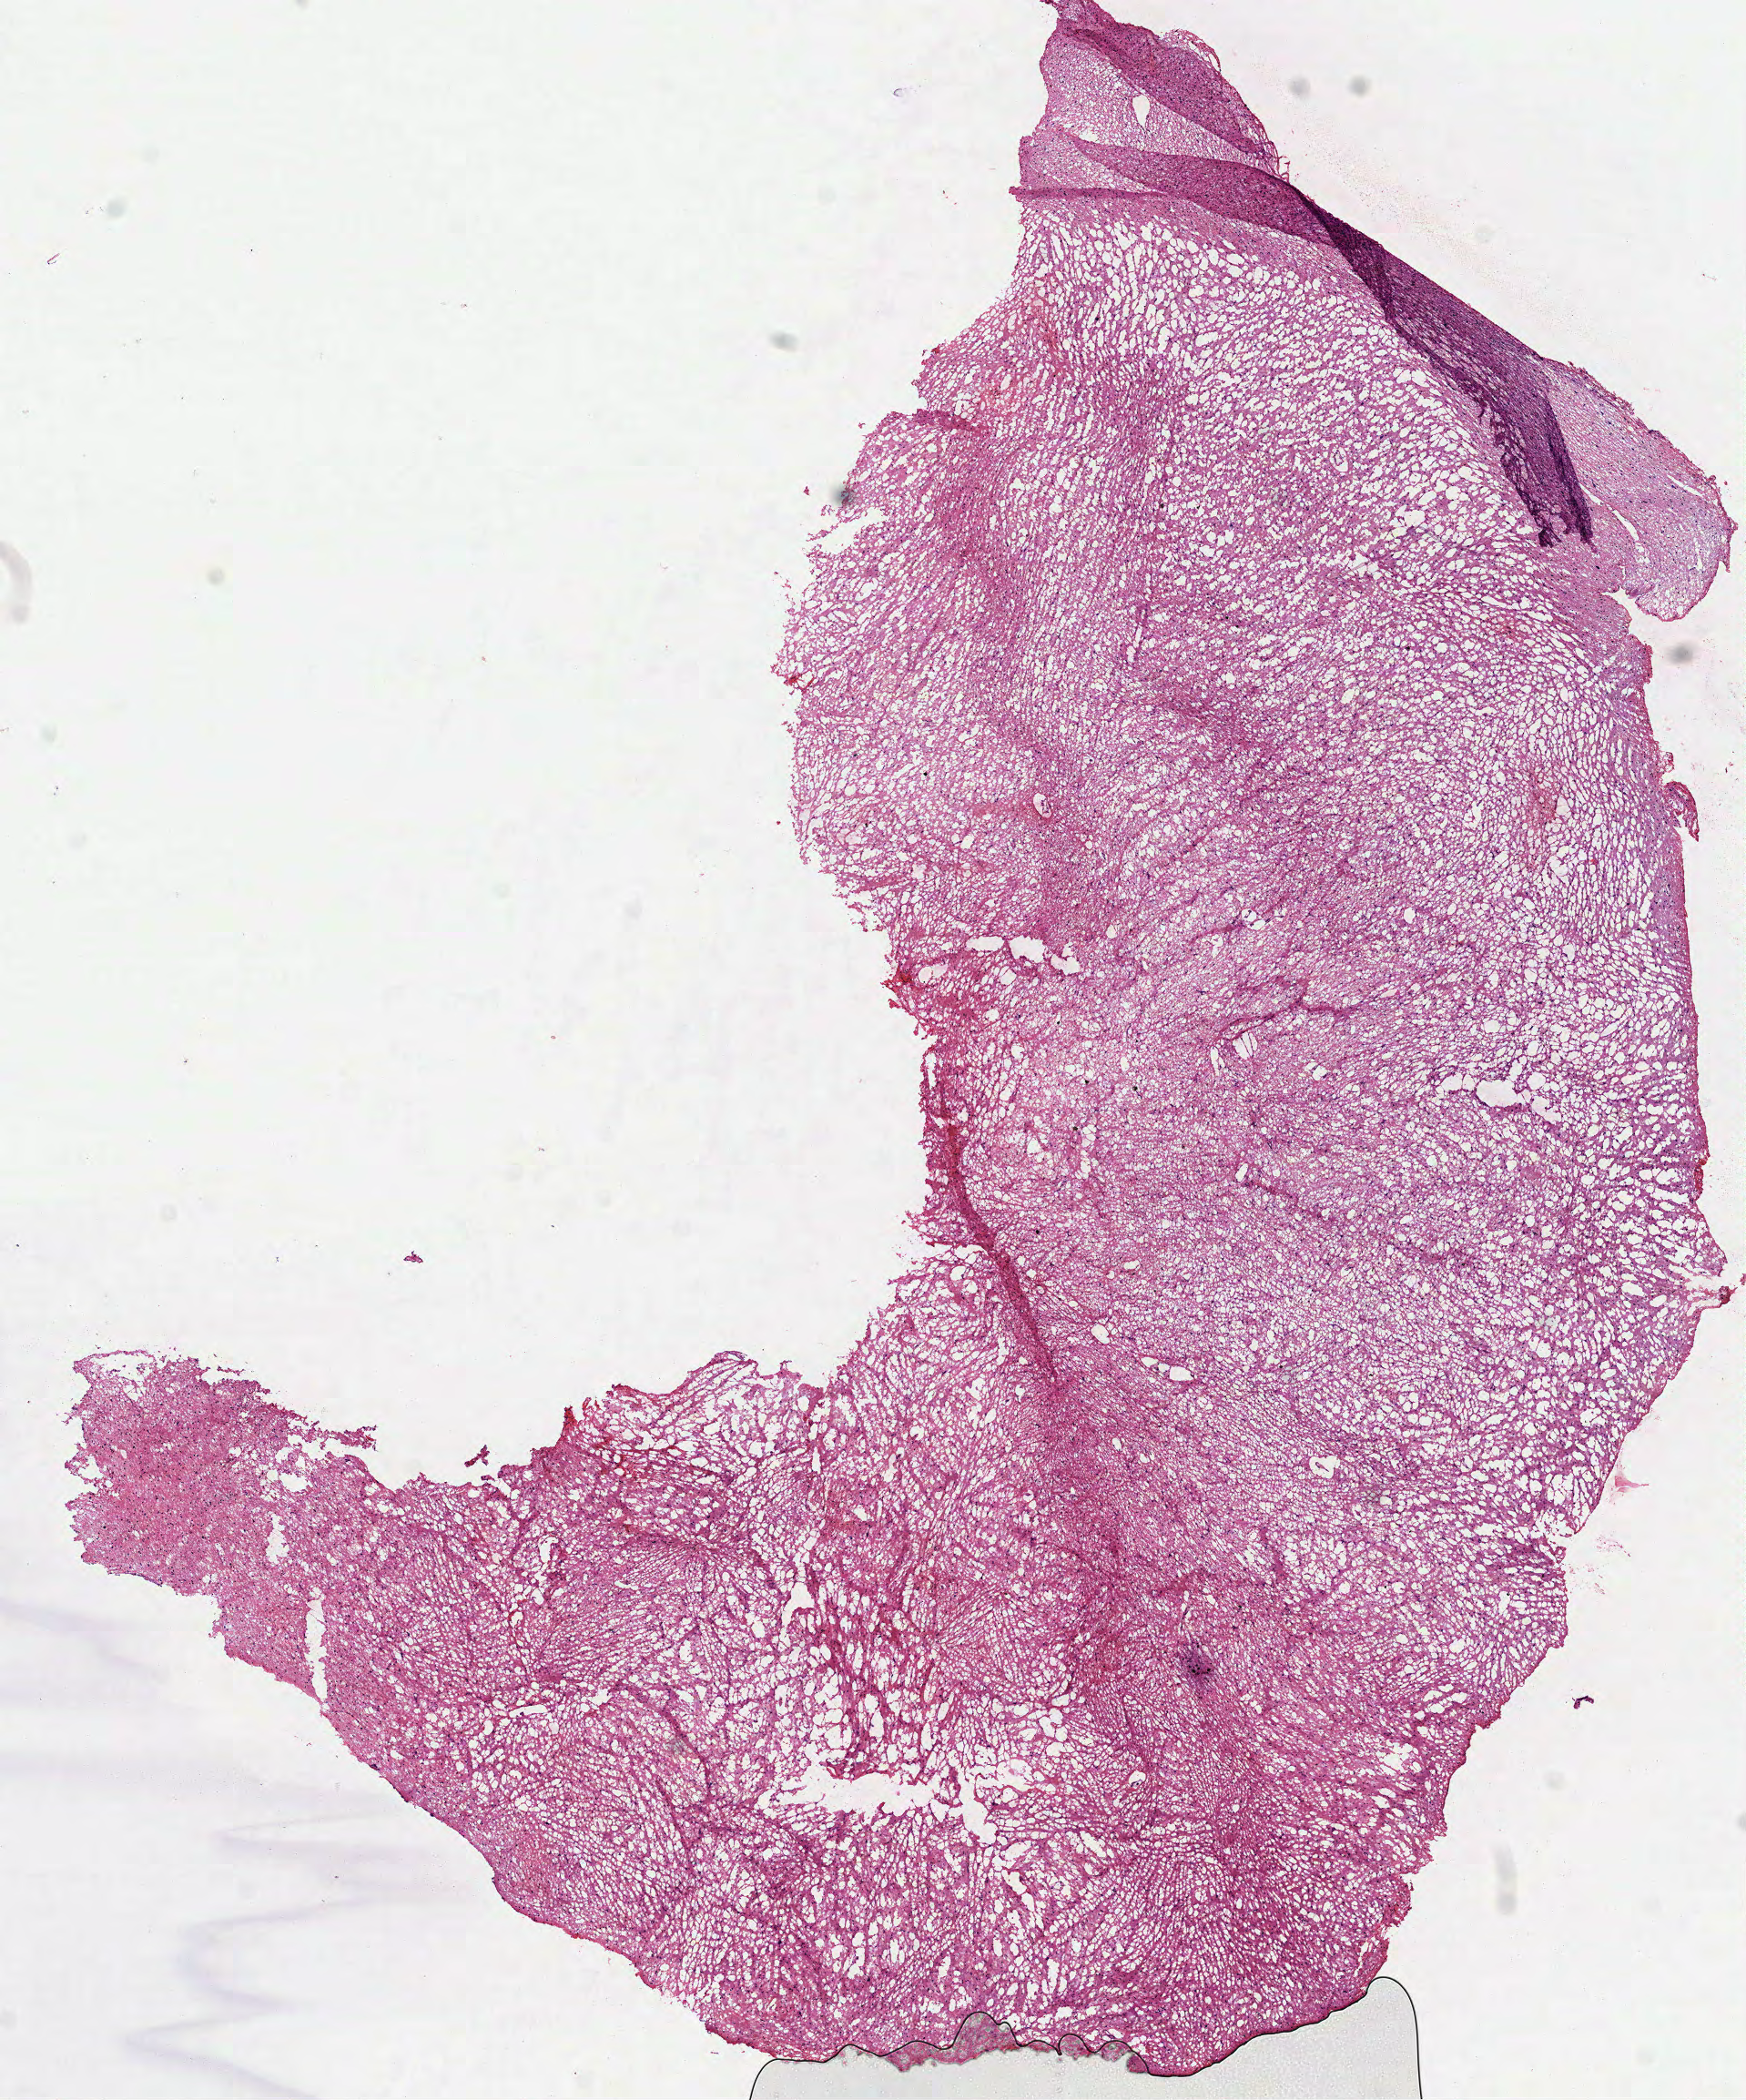
H&E whole-slide image, shown as a low-resolution overview of the whole scanned area (about 7.7 x 9.3 mm, acquisition: 40x scan); frozen section from the top of the tissue portion; primary tumour sample from the brain. Male, age 44 years at initial diagnosis. Histologic grade: G3 (poorly differentiated). Composition of this section per pathologist review: tumour cells 100%, tumour nuclei 60%, normal cells 0%, stromal cells 0%, necrosis 0%.
• pathologic diagnosis: Astrocytoma, anaplastic